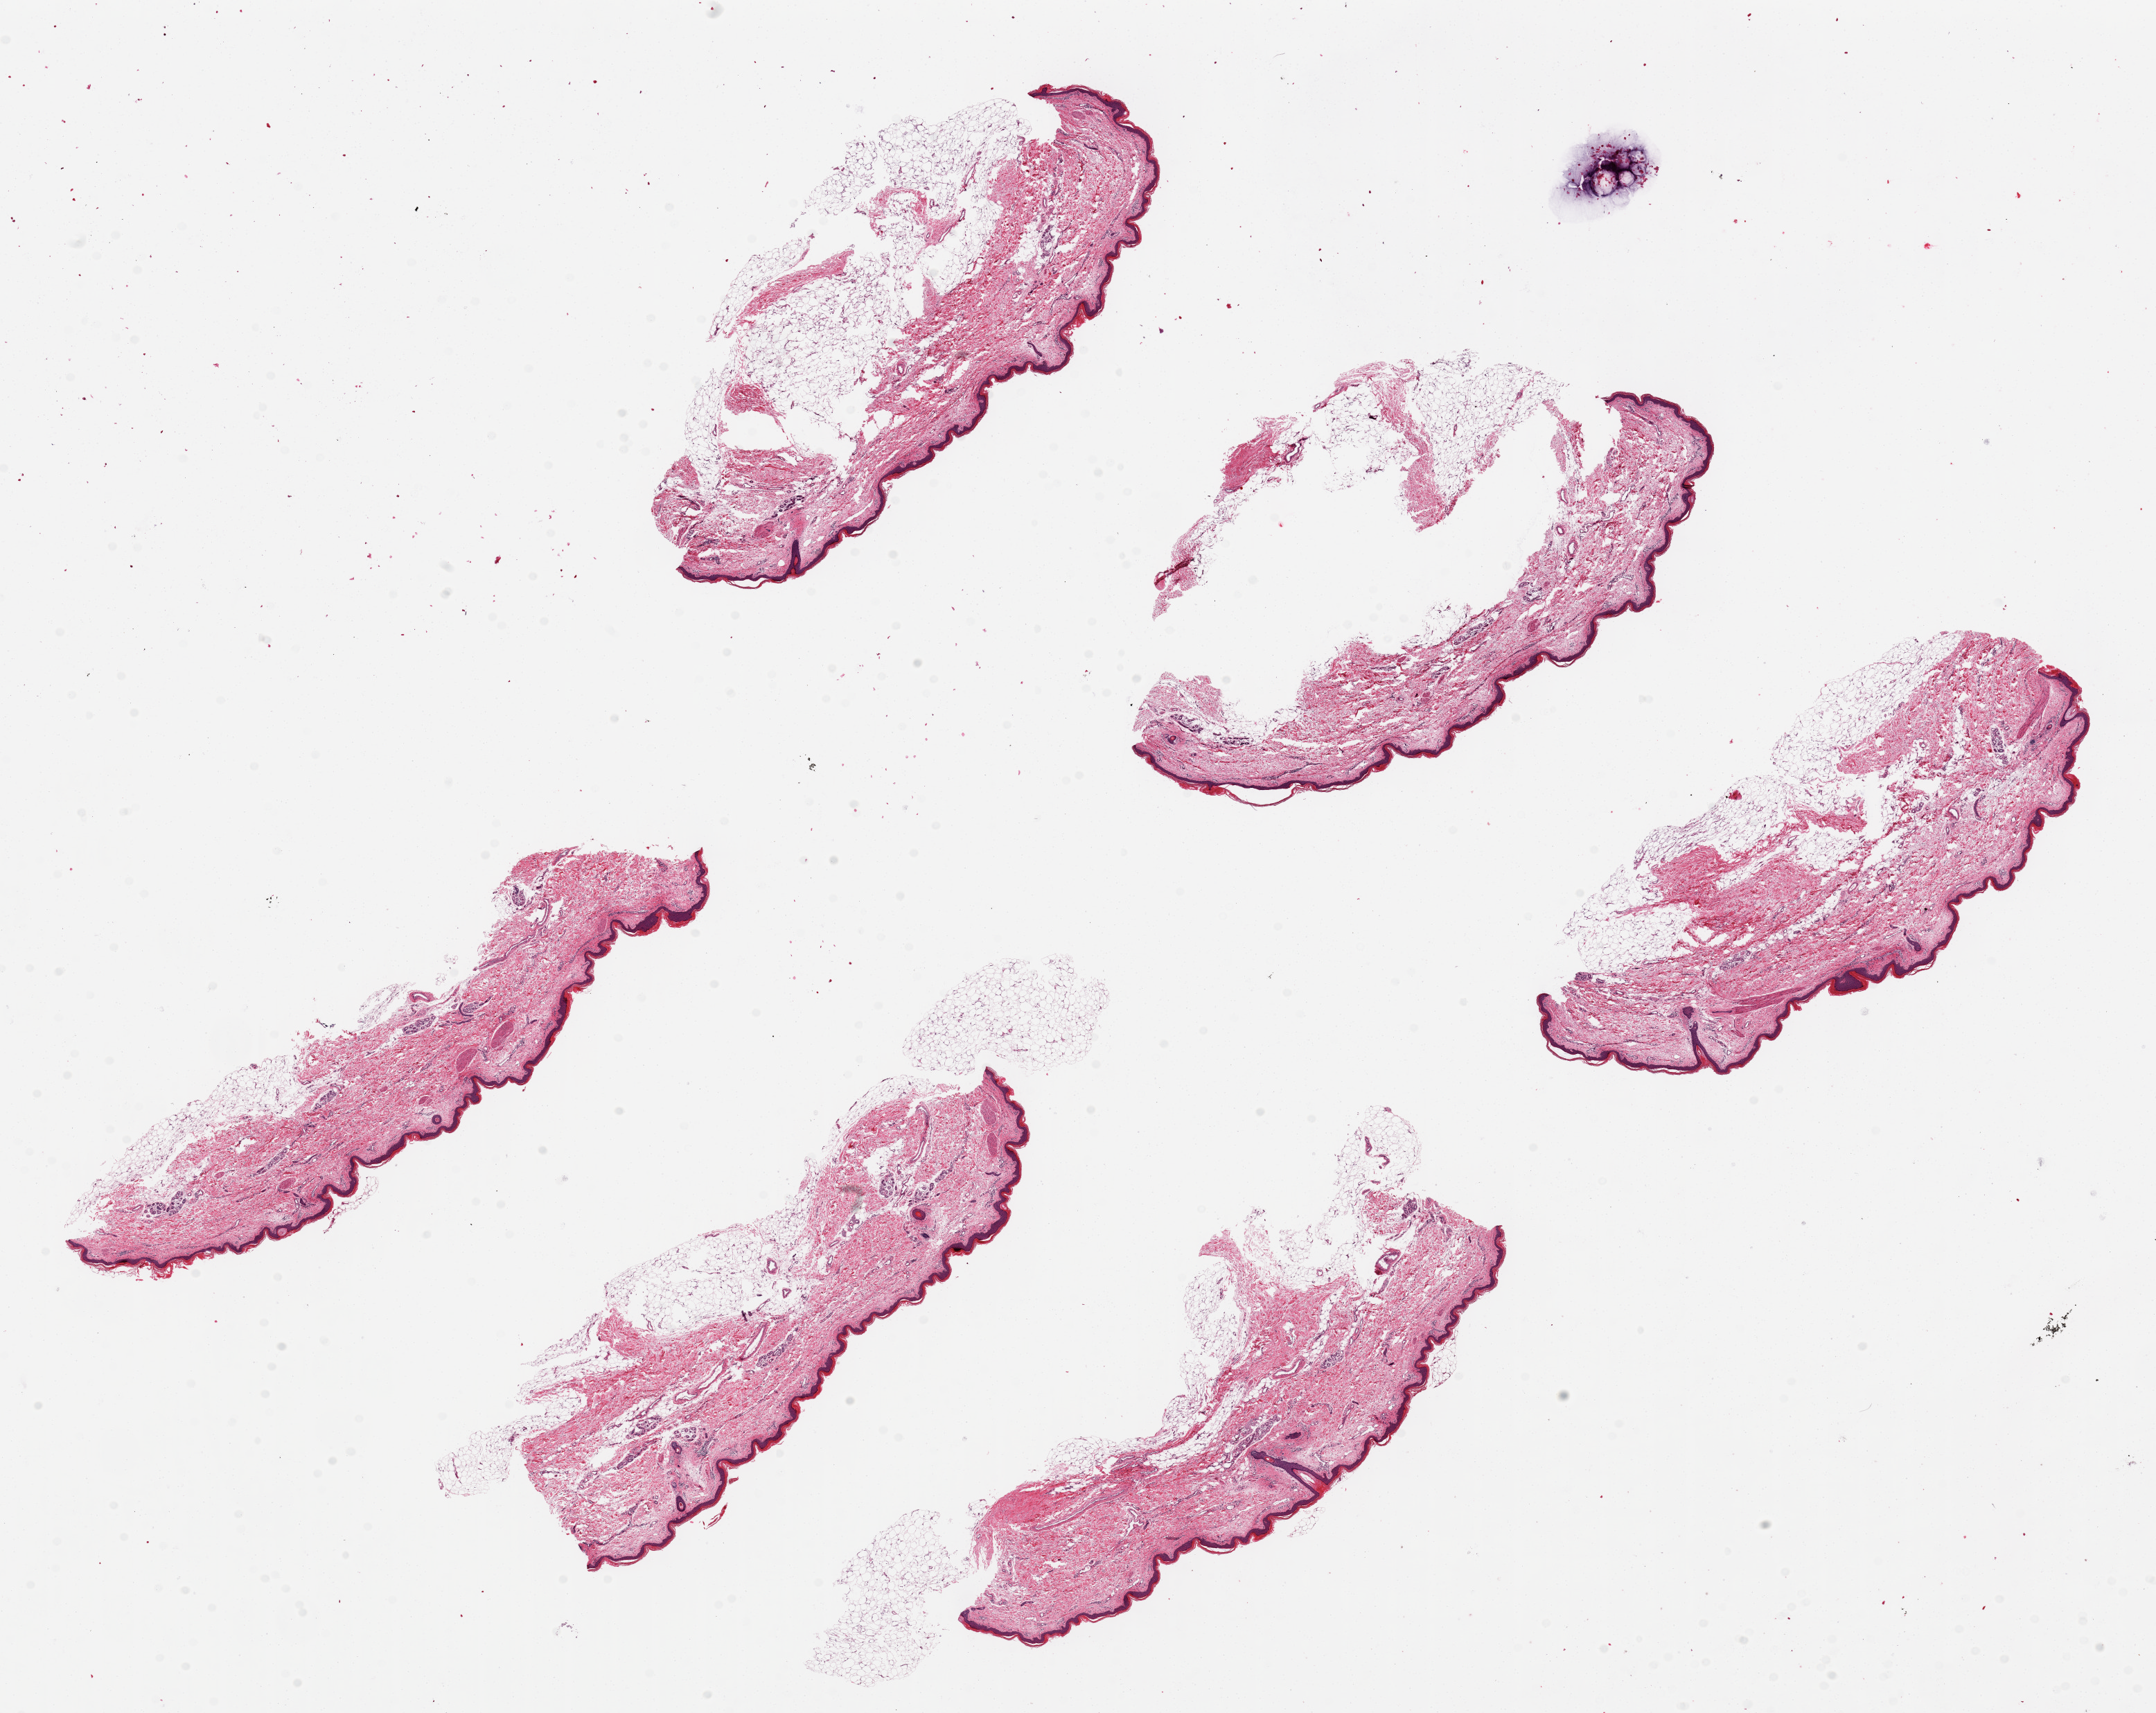
Digitized haematoxylin and eosin-stained section — a low-resolution overview of the entire scanned area, about 24.6 x 19.5 mm, PAXgene-fixed paraffin-embedded (PFPE) section, target tissue: skin of lower leg, tissue donor sample. Donor sex: female.
Pathologist's review note for this sample: 6 ~7x1.5mm pieces. Squamous epithelium is ~ 2-4% of thickness%.